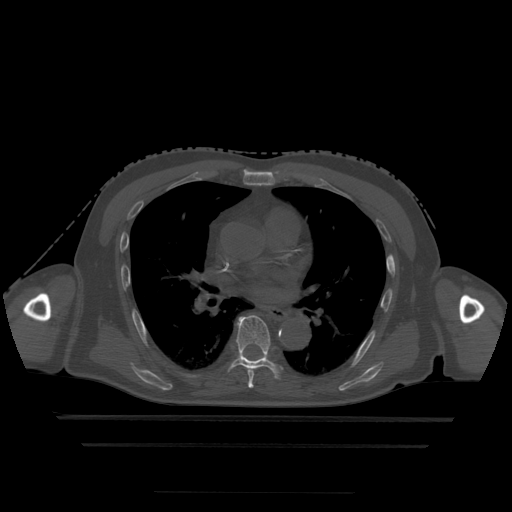
CT including the spine, one axial slice; bone window (W 1800 / L 400 HU); 1.25 mm slice thickness; 512 × 512 image matrix, field of view 436 × 436 mm. Patient age 68 years. Case-level facts recorded for this patient, not image findings: primary cancer: urothelial.
Structures marked on this image (semi-automatic segmentation, software-assisted and operator-edited):
- T5 vertebra: bounding box (x1, y1, x2, y2) in pixels: (248, 382, 253, 389)
- T6 vertebra: (247, 368, 256, 389)
- T7 vertebra: (230, 316, 279, 378)